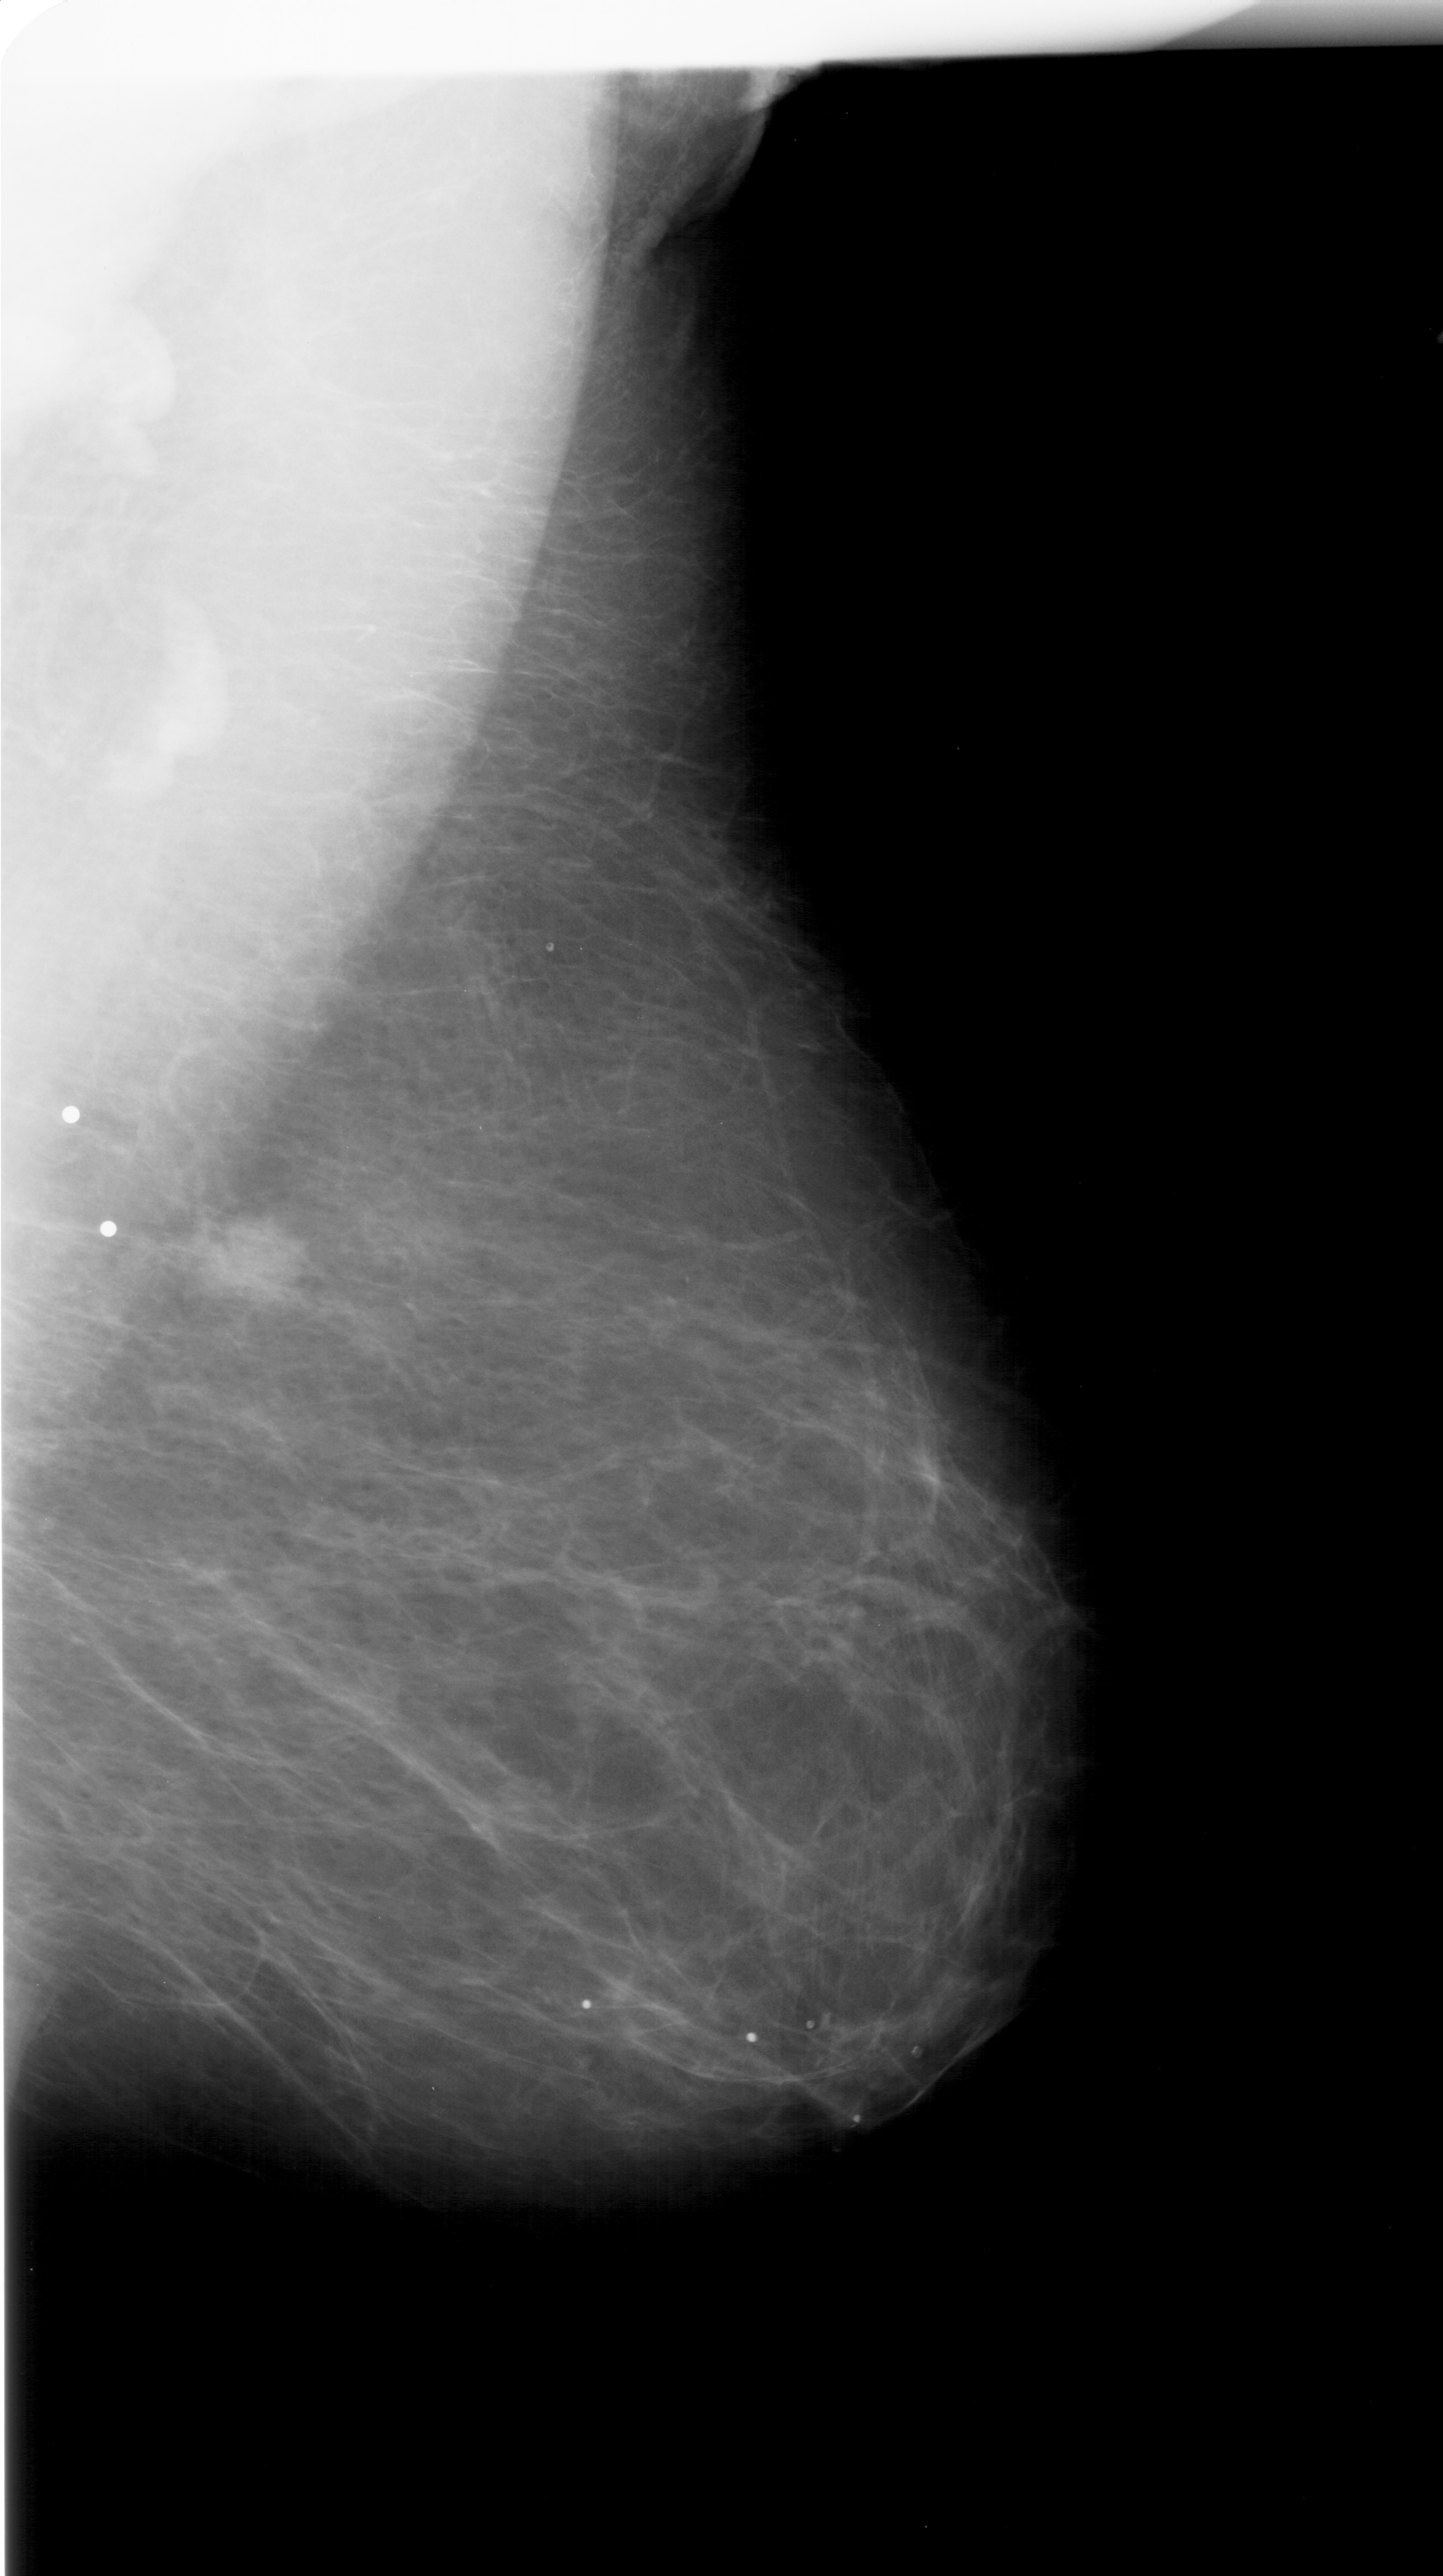
Mammogram (digitized film). Right breast. MLO view. BI-RADS breast density category 1 (scale 1–4). 1443 × 2576 image matrix.
Marked abnormalities (boxes around the expert regions of interest):
- mass, shape irregular, margins ill defined; BI-RADS assessment category 5; pathology (as recorded): malignant: bounding box (x1, y1, x2, y2) in pixels: (211, 1207, 312, 1312)